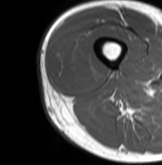
MRI of an extremity soft-tissue mass, one axial slice; slice 17 of 61 in the series (ordered by position); MR volume resampled by the dataset authors to the PET/CT grid (not the native acquisition matrix); 3.27 mm slice thickness; 162 × 165 image matrix, field of view 158 × 161 mm. Male patient. From the clinical record (not read from this slice): histological type: poorly differentiated synovial sarcoma; grade: high; site of the primary tumour: right buttock.
Outlined on this slice (expert contour drawn on MRI and transferred to this co-registered scan by the dataset authors):
- gross tumour volume including surrounding oedema: bounding box [x1, y1, x2, y2] px = [59, 45, 97, 85]